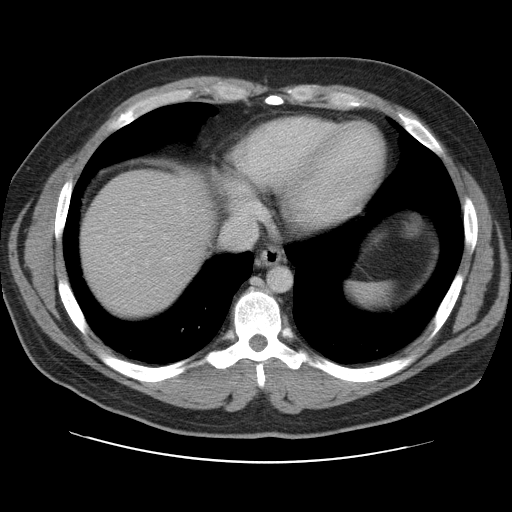
Contrast-enhanced abdominal CT, one axial slice; position 99 of 109 along the scan axis; 120 kVp; intravenous contrast given; soft-tissue window (W 400 / L 40 HU); 512 × 512 image matrix. Male patient, age 35 years. From the clinical record (not read from this slice): diagnosis: colorectal cancer liver metastases, imaged before liver resection; multiple liver metastases: yes; largest metastasis: 2.8 cm; disease in both lobes: yes.
Structures marked on this image (expert manual segmentation):
- hepatic veins: bounding box <133,230,255,272> (left, top, right, bottom; pixels)
- liver: <79,171,211,317>
- planned liver remnant (the part of the liver to remain after resection): <79,171,211,317>